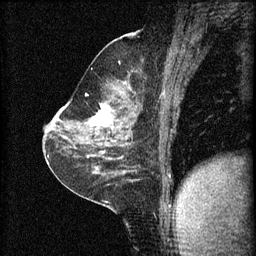
Breast MRI (dynamic contrast-enhanced), one sagittal slice; position 34 of 60 along the scan axis; 3 images stored at this slice position (order not interpretable as contrast timing); 1.5 T; TE 4.2 ms, TR 8.2 ms; 2 mm slice thickness; 256 × 256 image matrix, field of view 180 × 180 mm. Female patient, age 59 years.
Structures marked on this image (semi-automatic segmentation, software-assisted and operator-edited):
- analysis volume of interest (the breast-tissue region the enhancement analysis was run in; not a lesion): bounding box (x1, y1, x2, y2) in pixels: (78, 92, 137, 135)
- tumour enhancement mask (voxels above the 70 % enhancement threshold inside the analysis volume of interest): (90, 104, 113, 129)